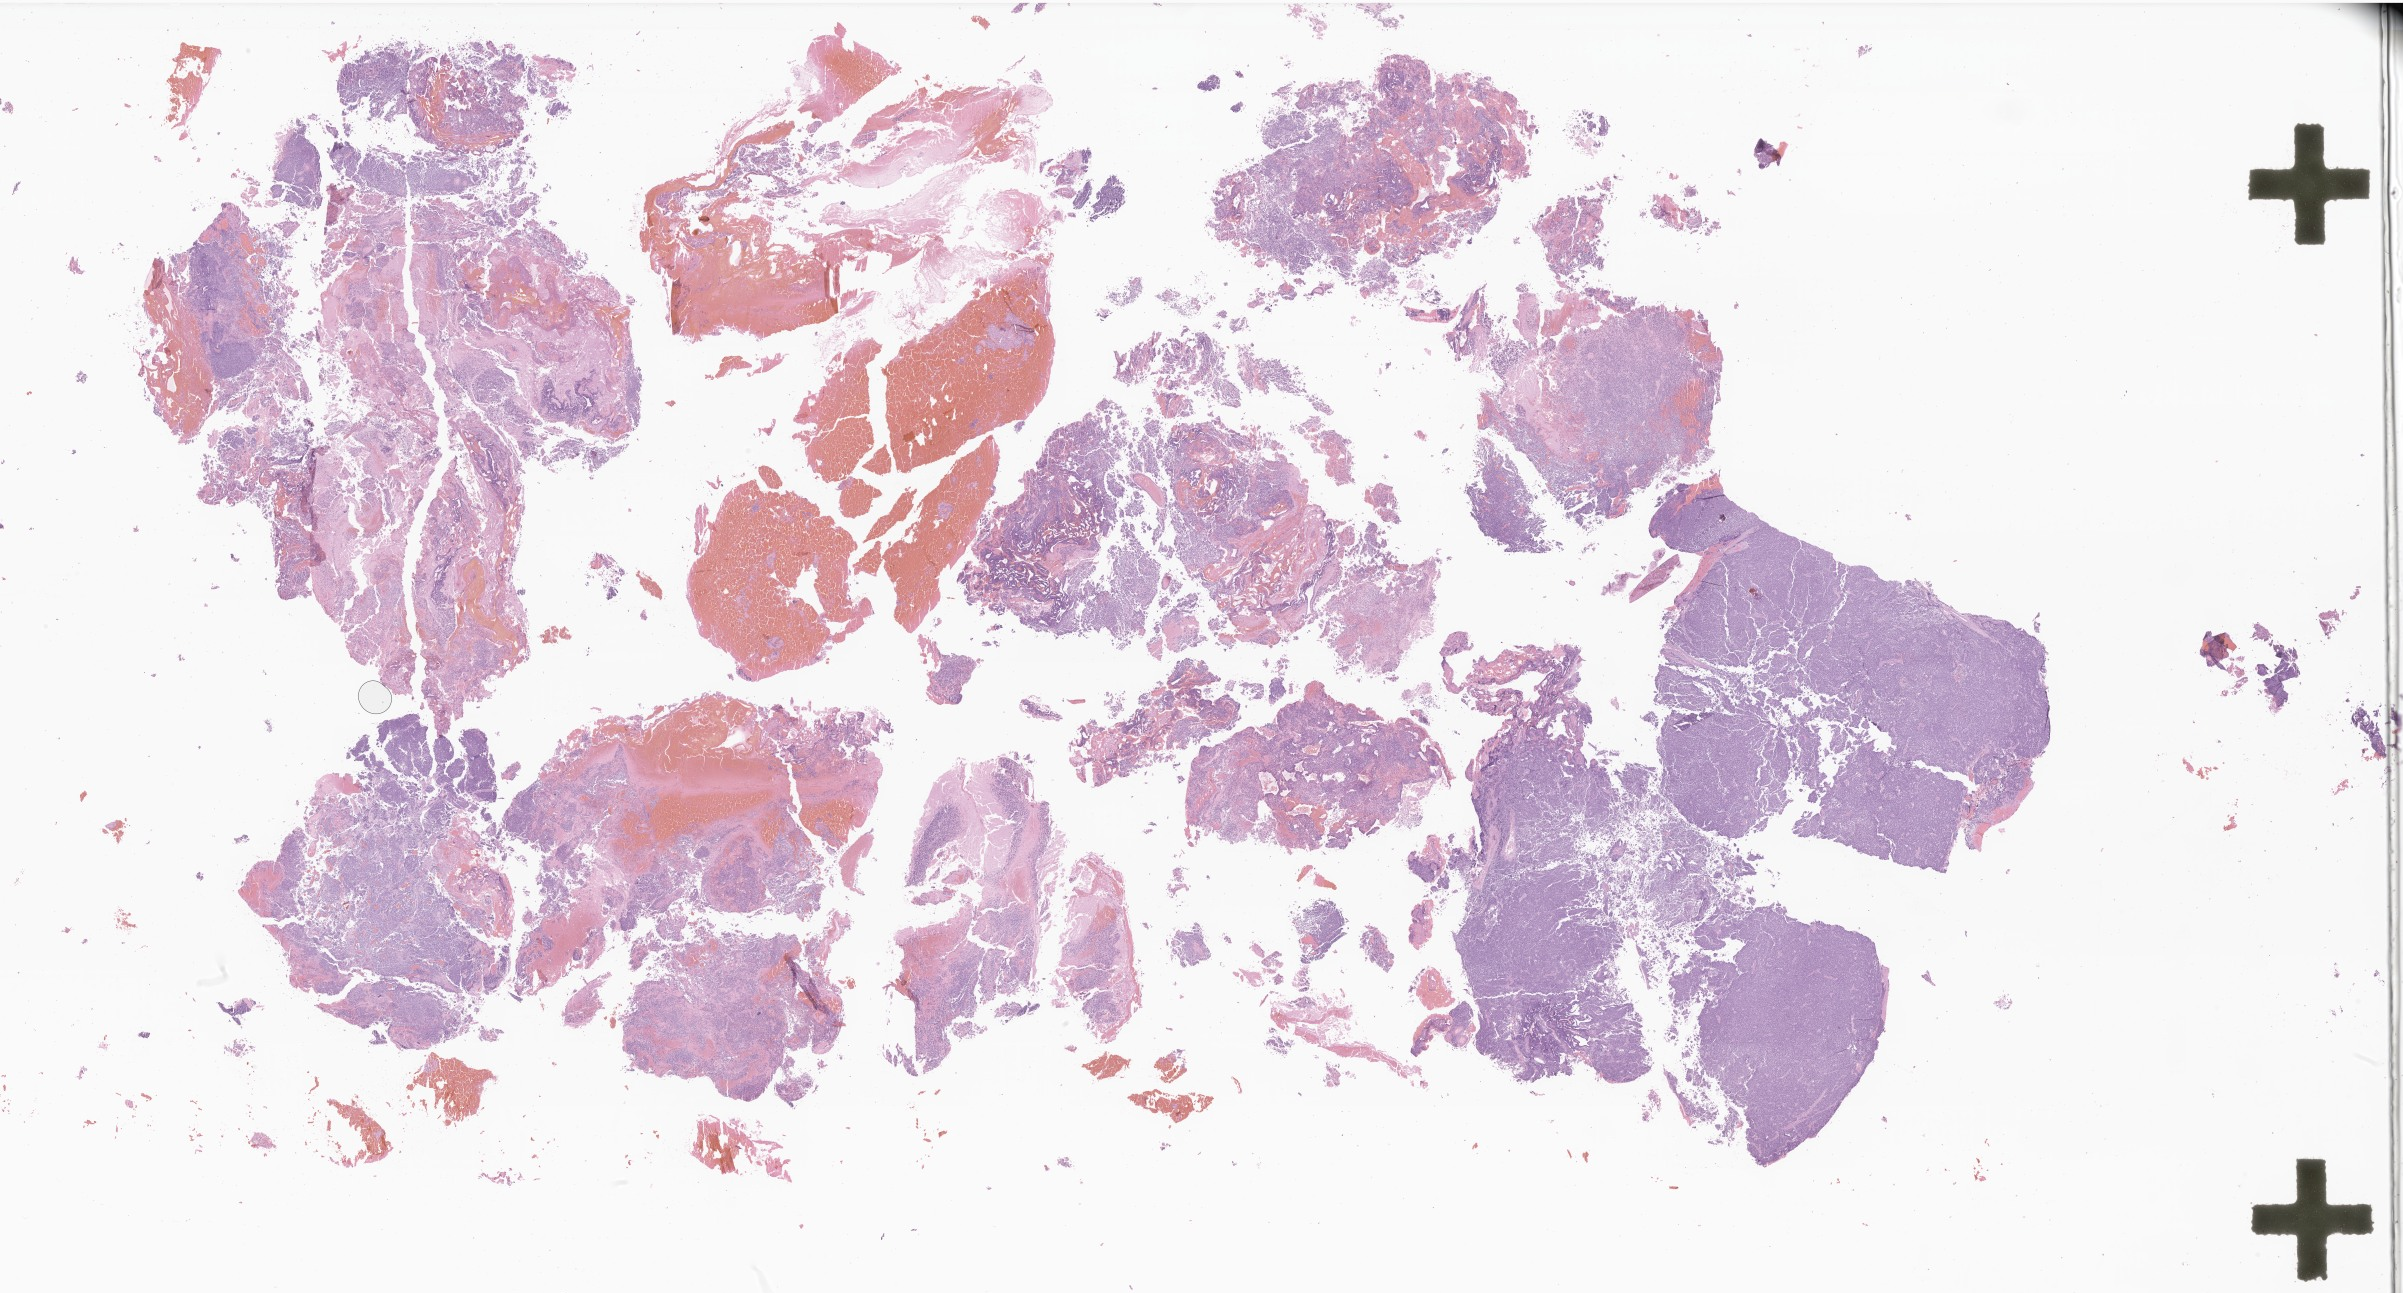
Whole-slide image, haematoxylin and eosin stain of tumor tissue from the brain — a low-resolution overview of the entire scanned area, about 40.5 x 21.8 mm; formalin-fixed, paraffin-embedded (FFPE) tissue. Patient: female, age 965 days (about 2.6 years).
- recorded diagnosis: Medulloblastoma, NOS